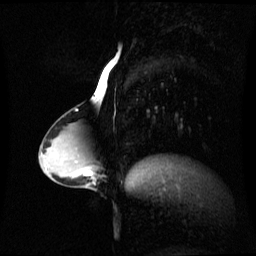
Breast MRI (dynamic contrast-enhanced), one sagittal slice; slice 30 of 60 in the series (ordered by position); dynamic contrast-enhanced series, image 2 of 3 at this slice position (ordered by acquisition); 1.5 T; TE 4.2 ms, TR 8.4 ms; 2.4 mm slice thickness; 256 × 256 image matrix, field of view 280 × 280 mm. Female patient, age 34 years. From the clinical record (not read from this slice): setting: breast cancer imaged before/during neoadjuvant chemotherapy; receptor status: triple-negative.
Outlined on this slice (semi-automatic segmentation, software-assisted and operator-edited):
- analysis volume of interest (the breast-tissue region the enhancement analysis was run in; not a lesion): bounding box [x1, y1, x2, y2] px = [57, 156, 94, 189]
- tumour enhancement mask (voxels above the 70 % enhancement threshold inside the analysis volume of interest): [85, 170, 92, 177]